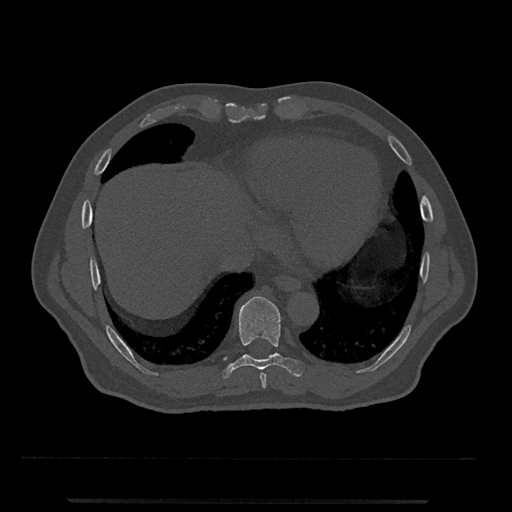
CT including the spine, one axial slice. Slice 574 of 797 in the series (ordered by position). Reconstruction kernel Br40s/3. 120 kVp. Bone window (W 1800 / L 400 HU). 0.5 mm slice thickness. 512 × 512 image matrix, field of view 419 × 419 mm. Patient: male, 63 years. From the clinical record (not read from this slice): primary cancer: prostate.
Annotated regions visible in this slice (semi-automatically segmented with operator editing):
- T8 vertebra: bounding box <259,373,267,388> (left, top, right, bottom; pixels)
- T9 vertebra: <221,296,305,378>